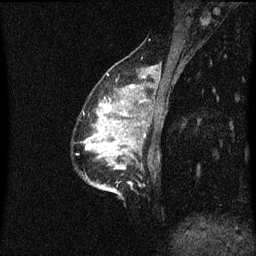
Breast MRI (dynamic contrast-enhanced), one sagittal slice; slice 14 of 60 in the series (ordered by position); dynamic contrast-enhanced series, image 2 of 3 at this slice position (ordered by acquisition); 1.5 T; TE 4.2 ms, TR 8.4 ms; 2 mm slice thickness; 256 × 256 image matrix, field of view 200 × 200 mm. Female patient, age 34 years. Case-level facts recorded for this patient, not image findings: setting: breast cancer imaged before/during neoadjuvant chemotherapy; receptor status: HR-positive, HER2-negative.
Outlined on this slice (semi-automatic segmentation, software-assisted and operator-edited):
- analysis volume of interest (the breast-tissue region the enhancement analysis was run in; not a lesion): bounding box (x1, y1, x2, y2) in pixels: (85, 78, 146, 195)
- tumour enhancement mask (voxels above the 70 % enhancement threshold inside the analysis volume of interest): (88, 144, 92, 147)